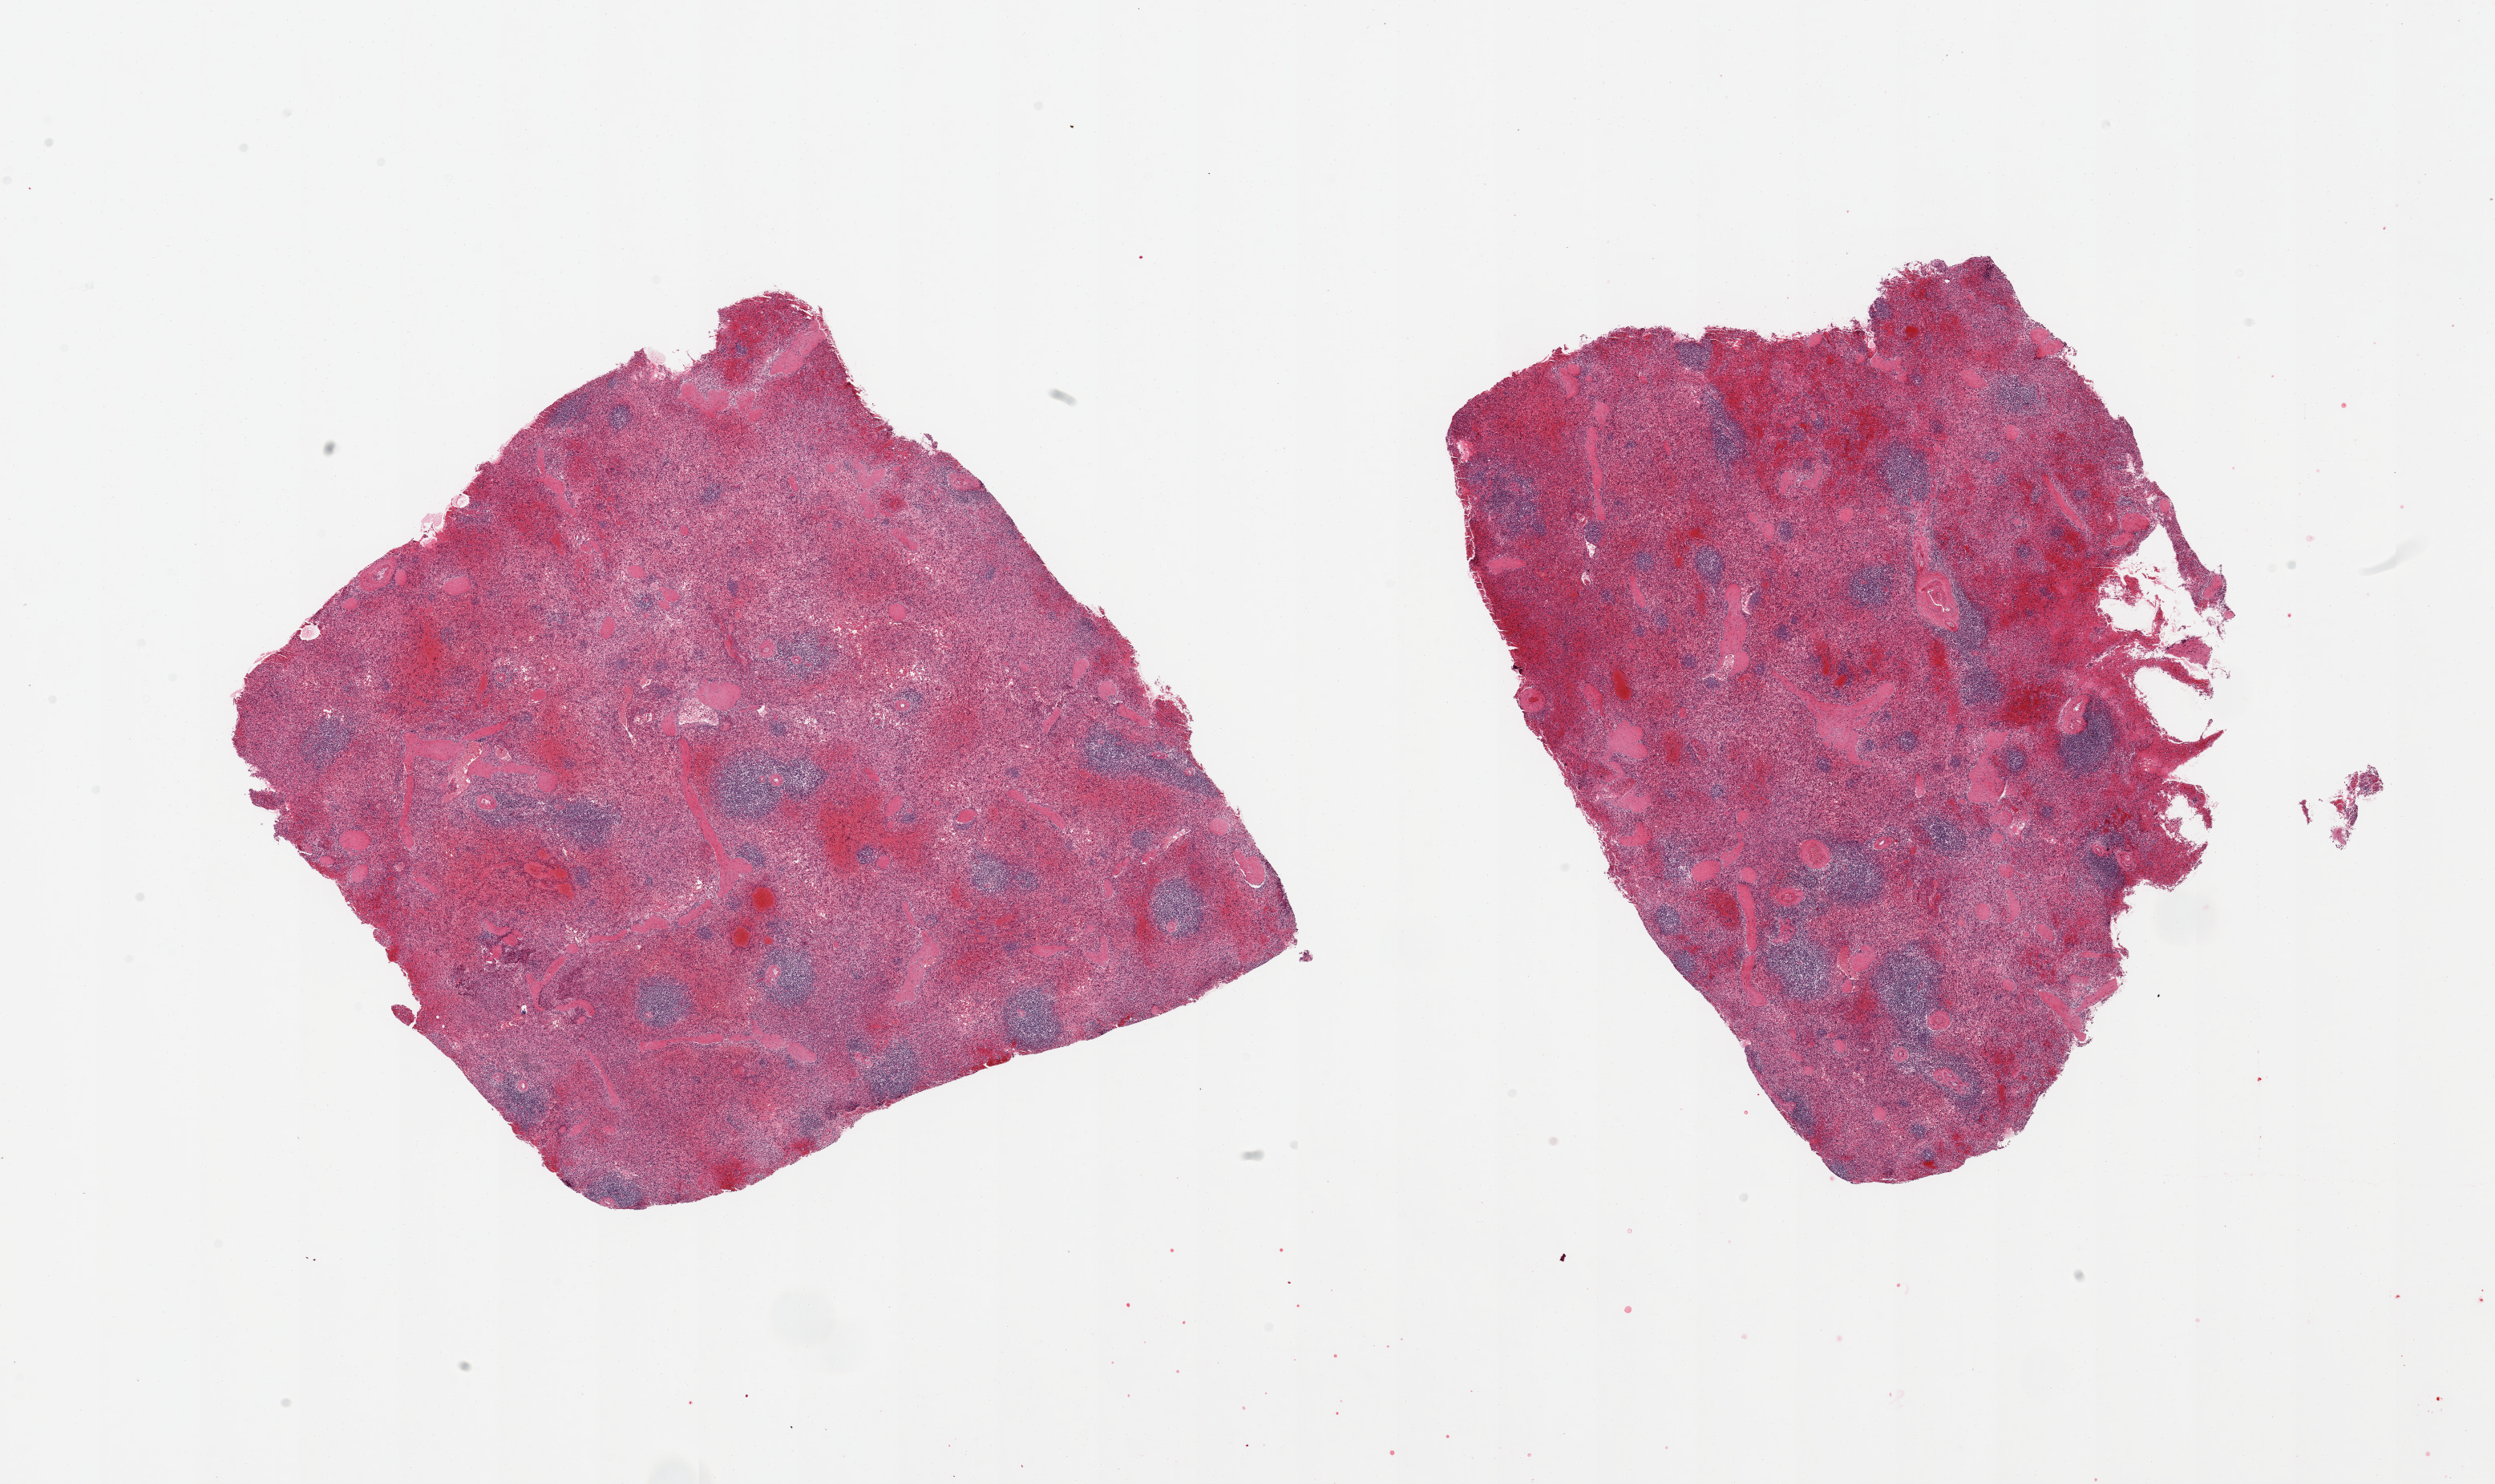
Digitized H&E-stained section, whole scanned area (about 24.6 x 14.6 mm, acquisition: 20x scan) shown as a low-resolution overview. PAXgene-fixed, paraffin-embedded tissue. Target tissue: spleen. Donor tissue sample. Donor sex: male.
Reviewer comment on this tissue sample: 2 pieces, moderate congestion.